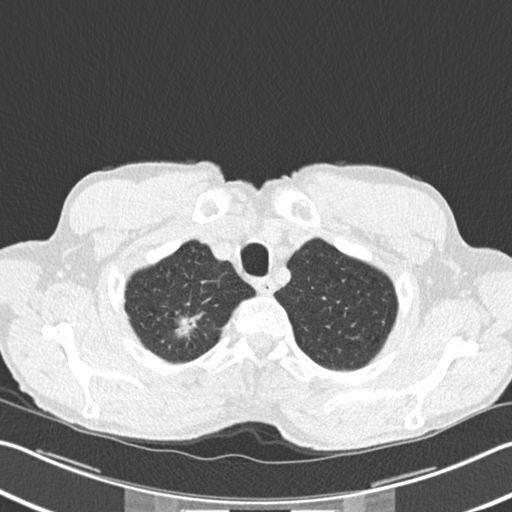
Low-dose screening chest CT, one axial slice. Slice 198 of 220 in the series (ordered by position). 120 kVp. Lung window (W 1500 / L -600 HU). 2 mm slice thickness. 512 × 512 image matrix.
Structures marked on this image (outlined manually by an expert reader):
- lesion 1 (tumor, upper lobe of right lung): bounding box [x1, y1, x2, y2] px = [176, 315, 201, 336]